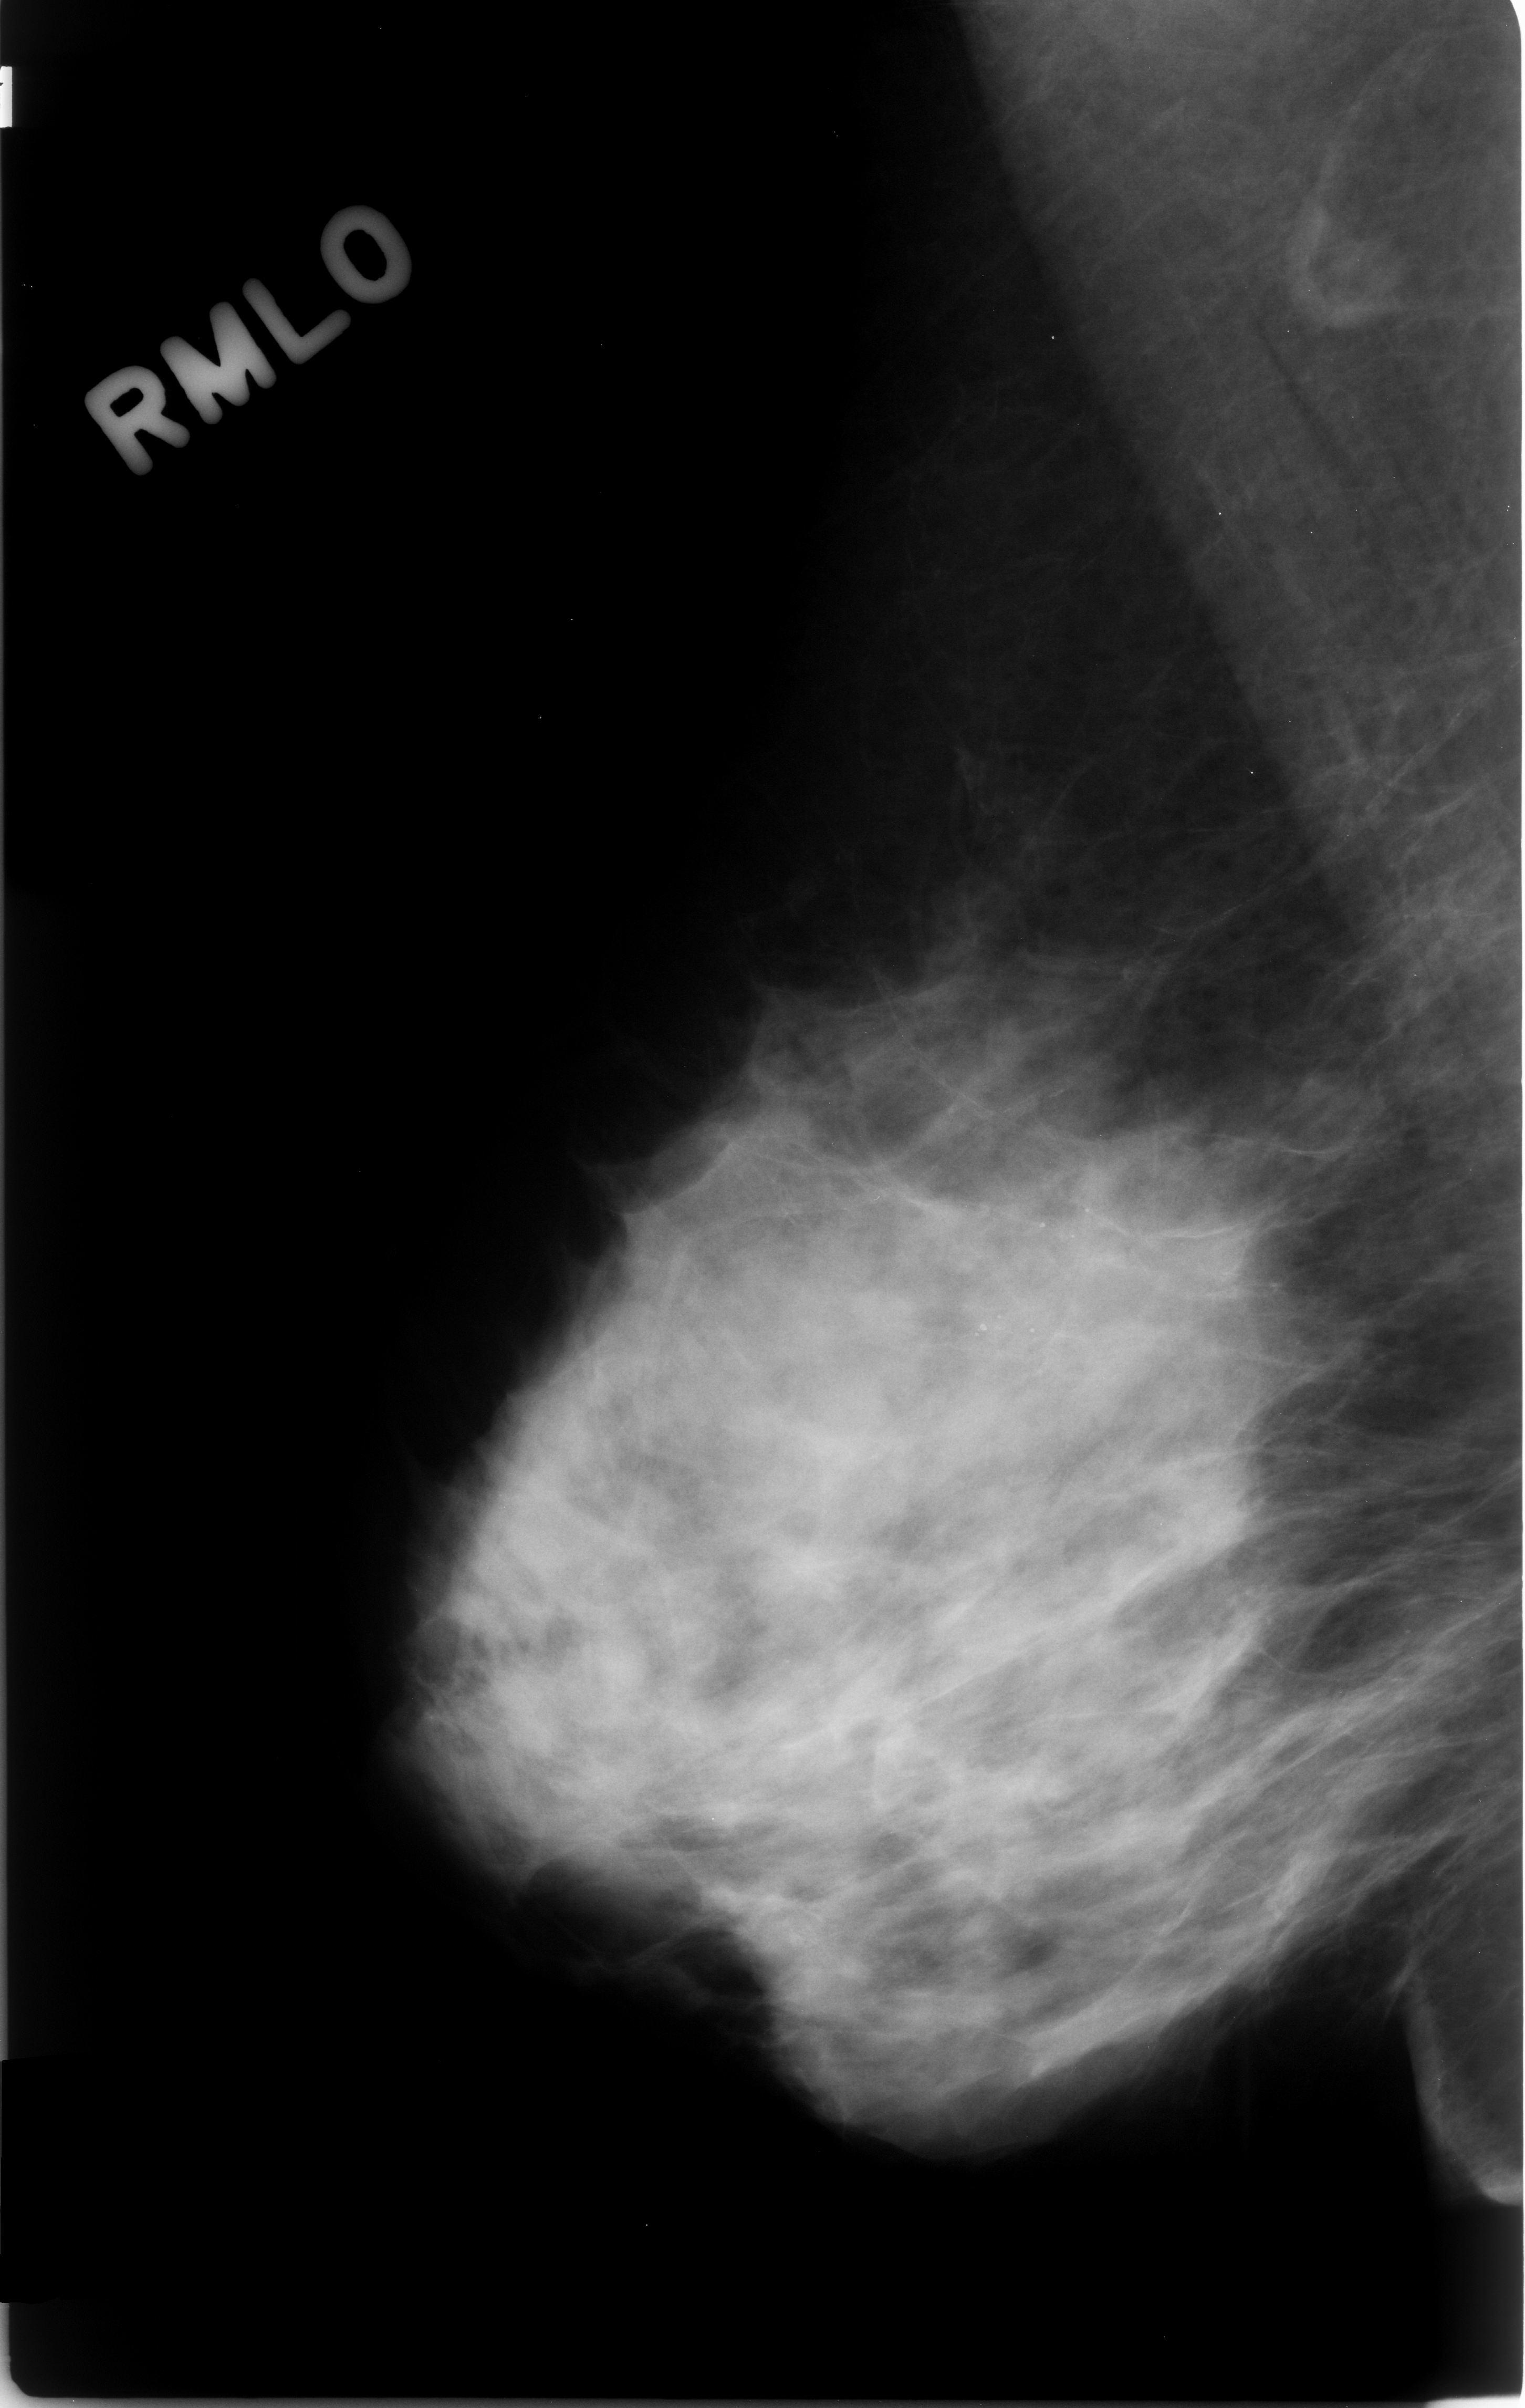
Digitized screen-film mammogram, right breast, MLO view.
- Calcifications, morphology round and regular, distribution clustered; BI-RADS assessment category 4; pathology result (as recorded, not read from the image): benign.